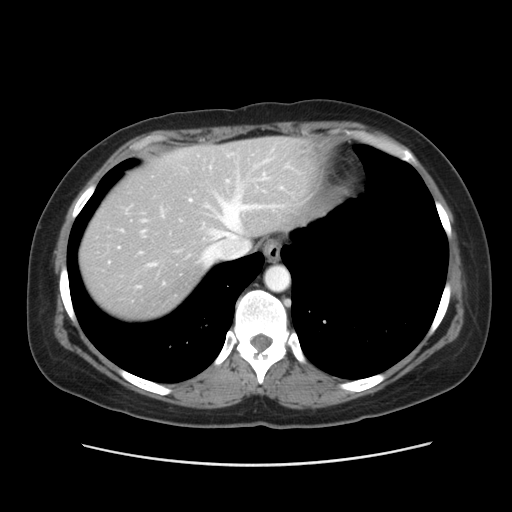
Contrast-enhanced abdominal CT, one axial slice. Slice 43 of 52 in the series (ordered by position). Reconstruction kernel STANDARD. Intravenous contrast given. Soft-tissue window (W 400 / L 40 HU). 5 mm slice thickness. 512 × 512 image matrix, field of view 362 × 362 mm. Female patient, age 48 years. From the clinical record (not read from this slice): diagnosis: colorectal cancer liver metastases, imaged before liver resection; multiple liver metastases: yes; largest metastasis: 4.5 cm.
Annotated regions visible in this slice (manually delineated by an expert):
- hepatic veins: bounding box [x1, y1, x2, y2] px = [118, 154, 282, 286]
- liver: [79, 138, 309, 317]
- planned liver remnant (the part of the liver to remain after resection): [156, 138, 309, 237]